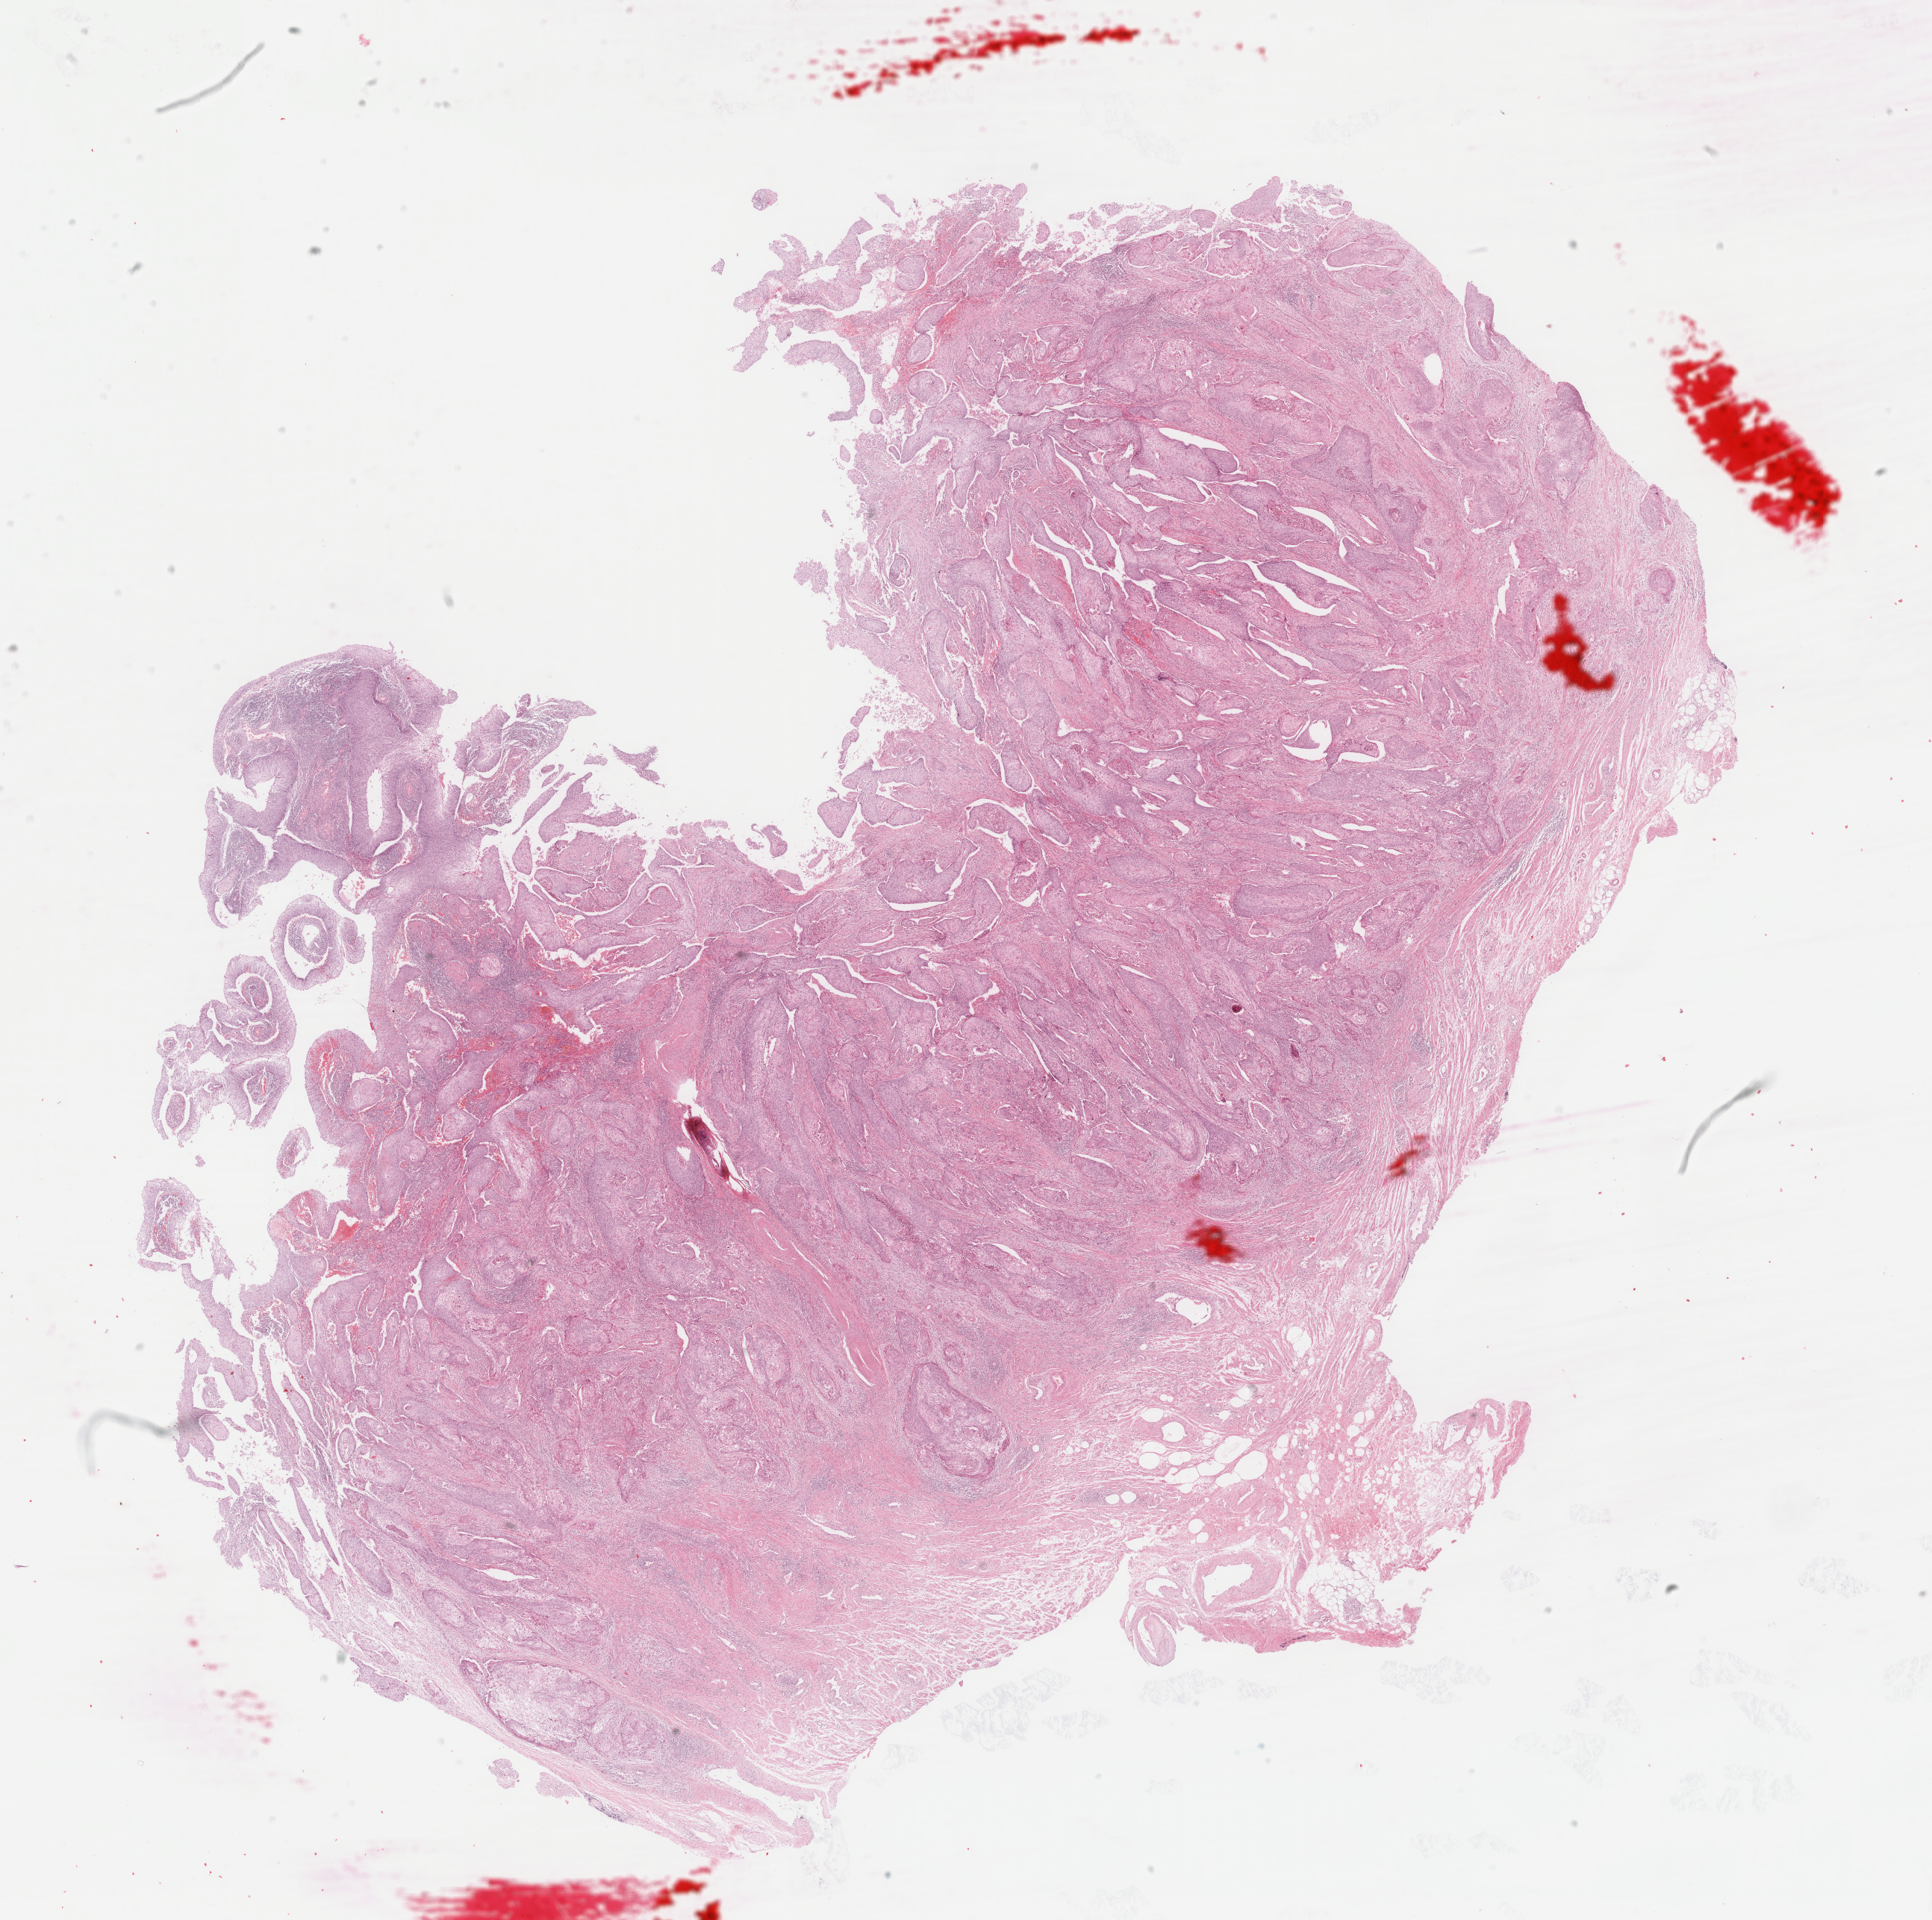
Digitized H&E tissue section (whole slide) — a low-resolution overview of the entire scanned area, about 20.5 x 20.4 mm, FFPE section, cervix, primary tumour sample. Female patient; age at initial diagnosis 68 years. Histologic grade: G1 (well differentiated).
FIGO stage: IB. Lymph nodes positive (case pathology): 0 of 9 examined. Pathologic diagnosis: Squamous cell carcinoma, NOS (cervix uteri).